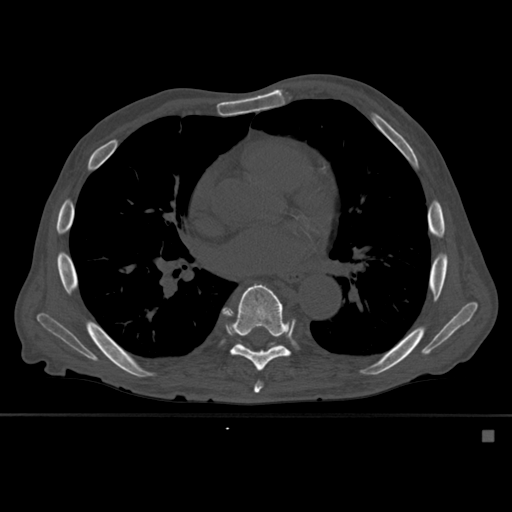
CT including the spine, one axial slice. Slice 350 of 527 in the series (ordered by position). Bone window (W 1800 / L 400 HU). 1.5 mm slice thickness. 512 × 512 image matrix, field of view 373 × 373 mm. Male patient, age 78 years. From the clinical record (not read from this slice): primary cancer: prostate.
Outlined on this slice (semi-automatically segmented with operator editing):
- T7 vertebra: bounding box <226,291,263,393> (left, top, right, bottom; pixels)
- T8 vertebra: <230,283,292,372>
- T9 vertebra: <236,340,281,350>